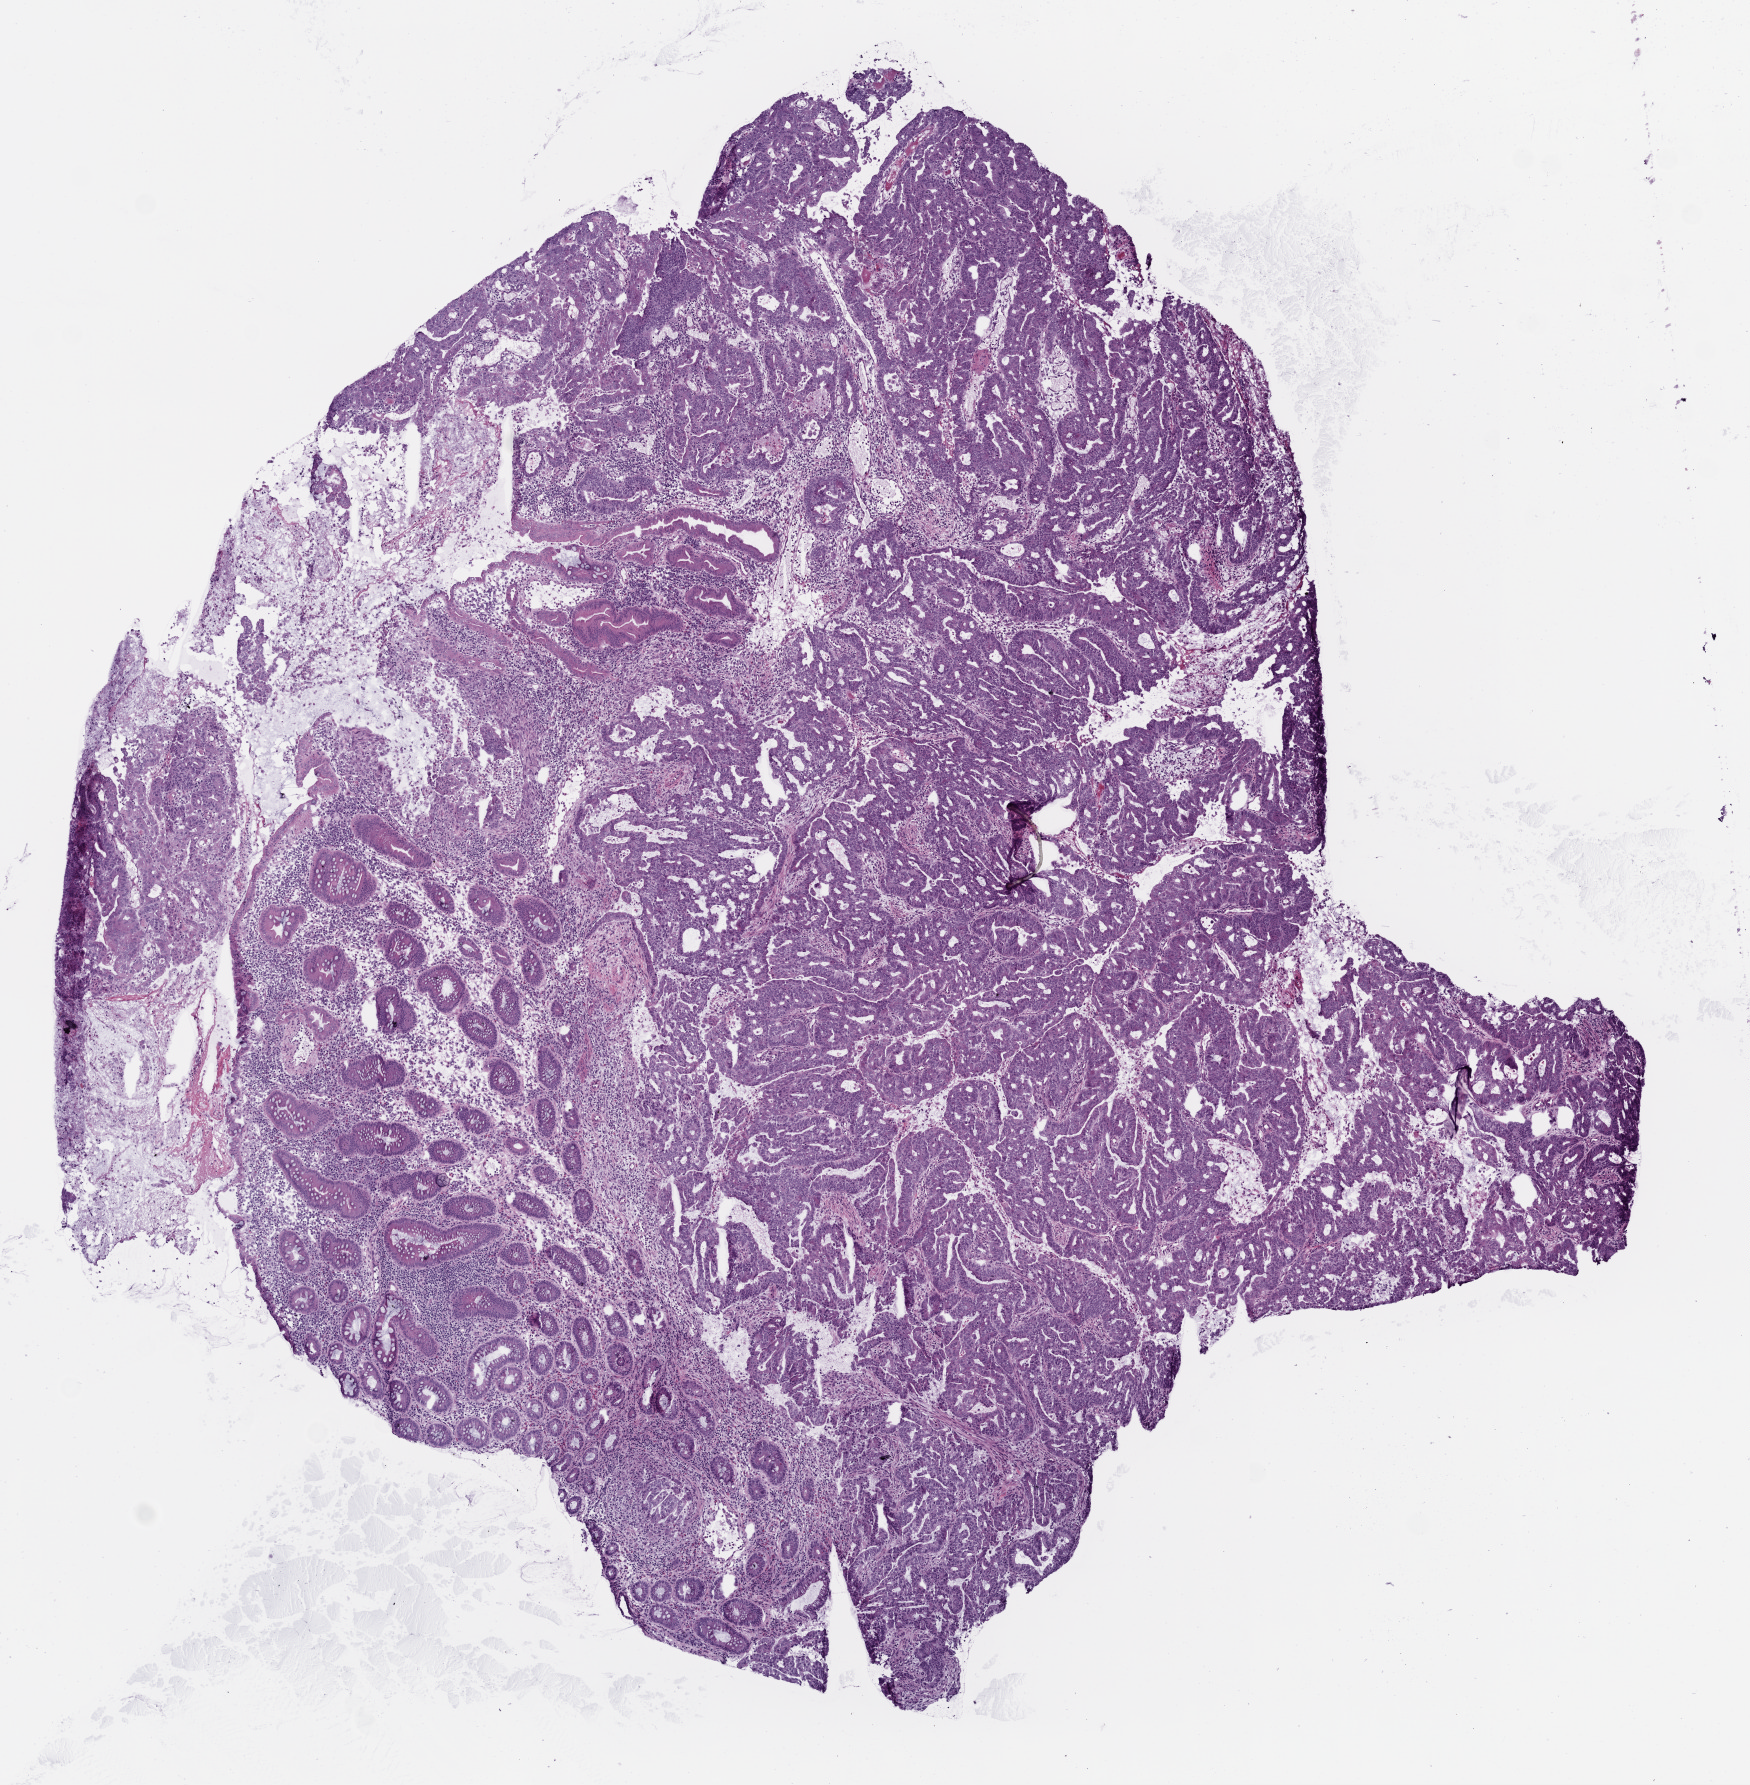
Whole-slide histology image, H&E-stained — shown as a low-resolution overview of the whole scanned area (about 7.0 x 7.2 mm), frozen section from the top of the tissue portion, primary tumour sample from the colon. Female patient; age at initial diagnosis 65 years. Slide review estimates, as recorded: tumour cells 82%, tumour nuclei 80%, normal cells 15%, stromal cells 10%, necrosis 3%.
Pathologic diagnosis: Adenocarcinoma, NOS (ascending colon). TNM: T3 N1a M1. AJCC pathologic stage: IVA.